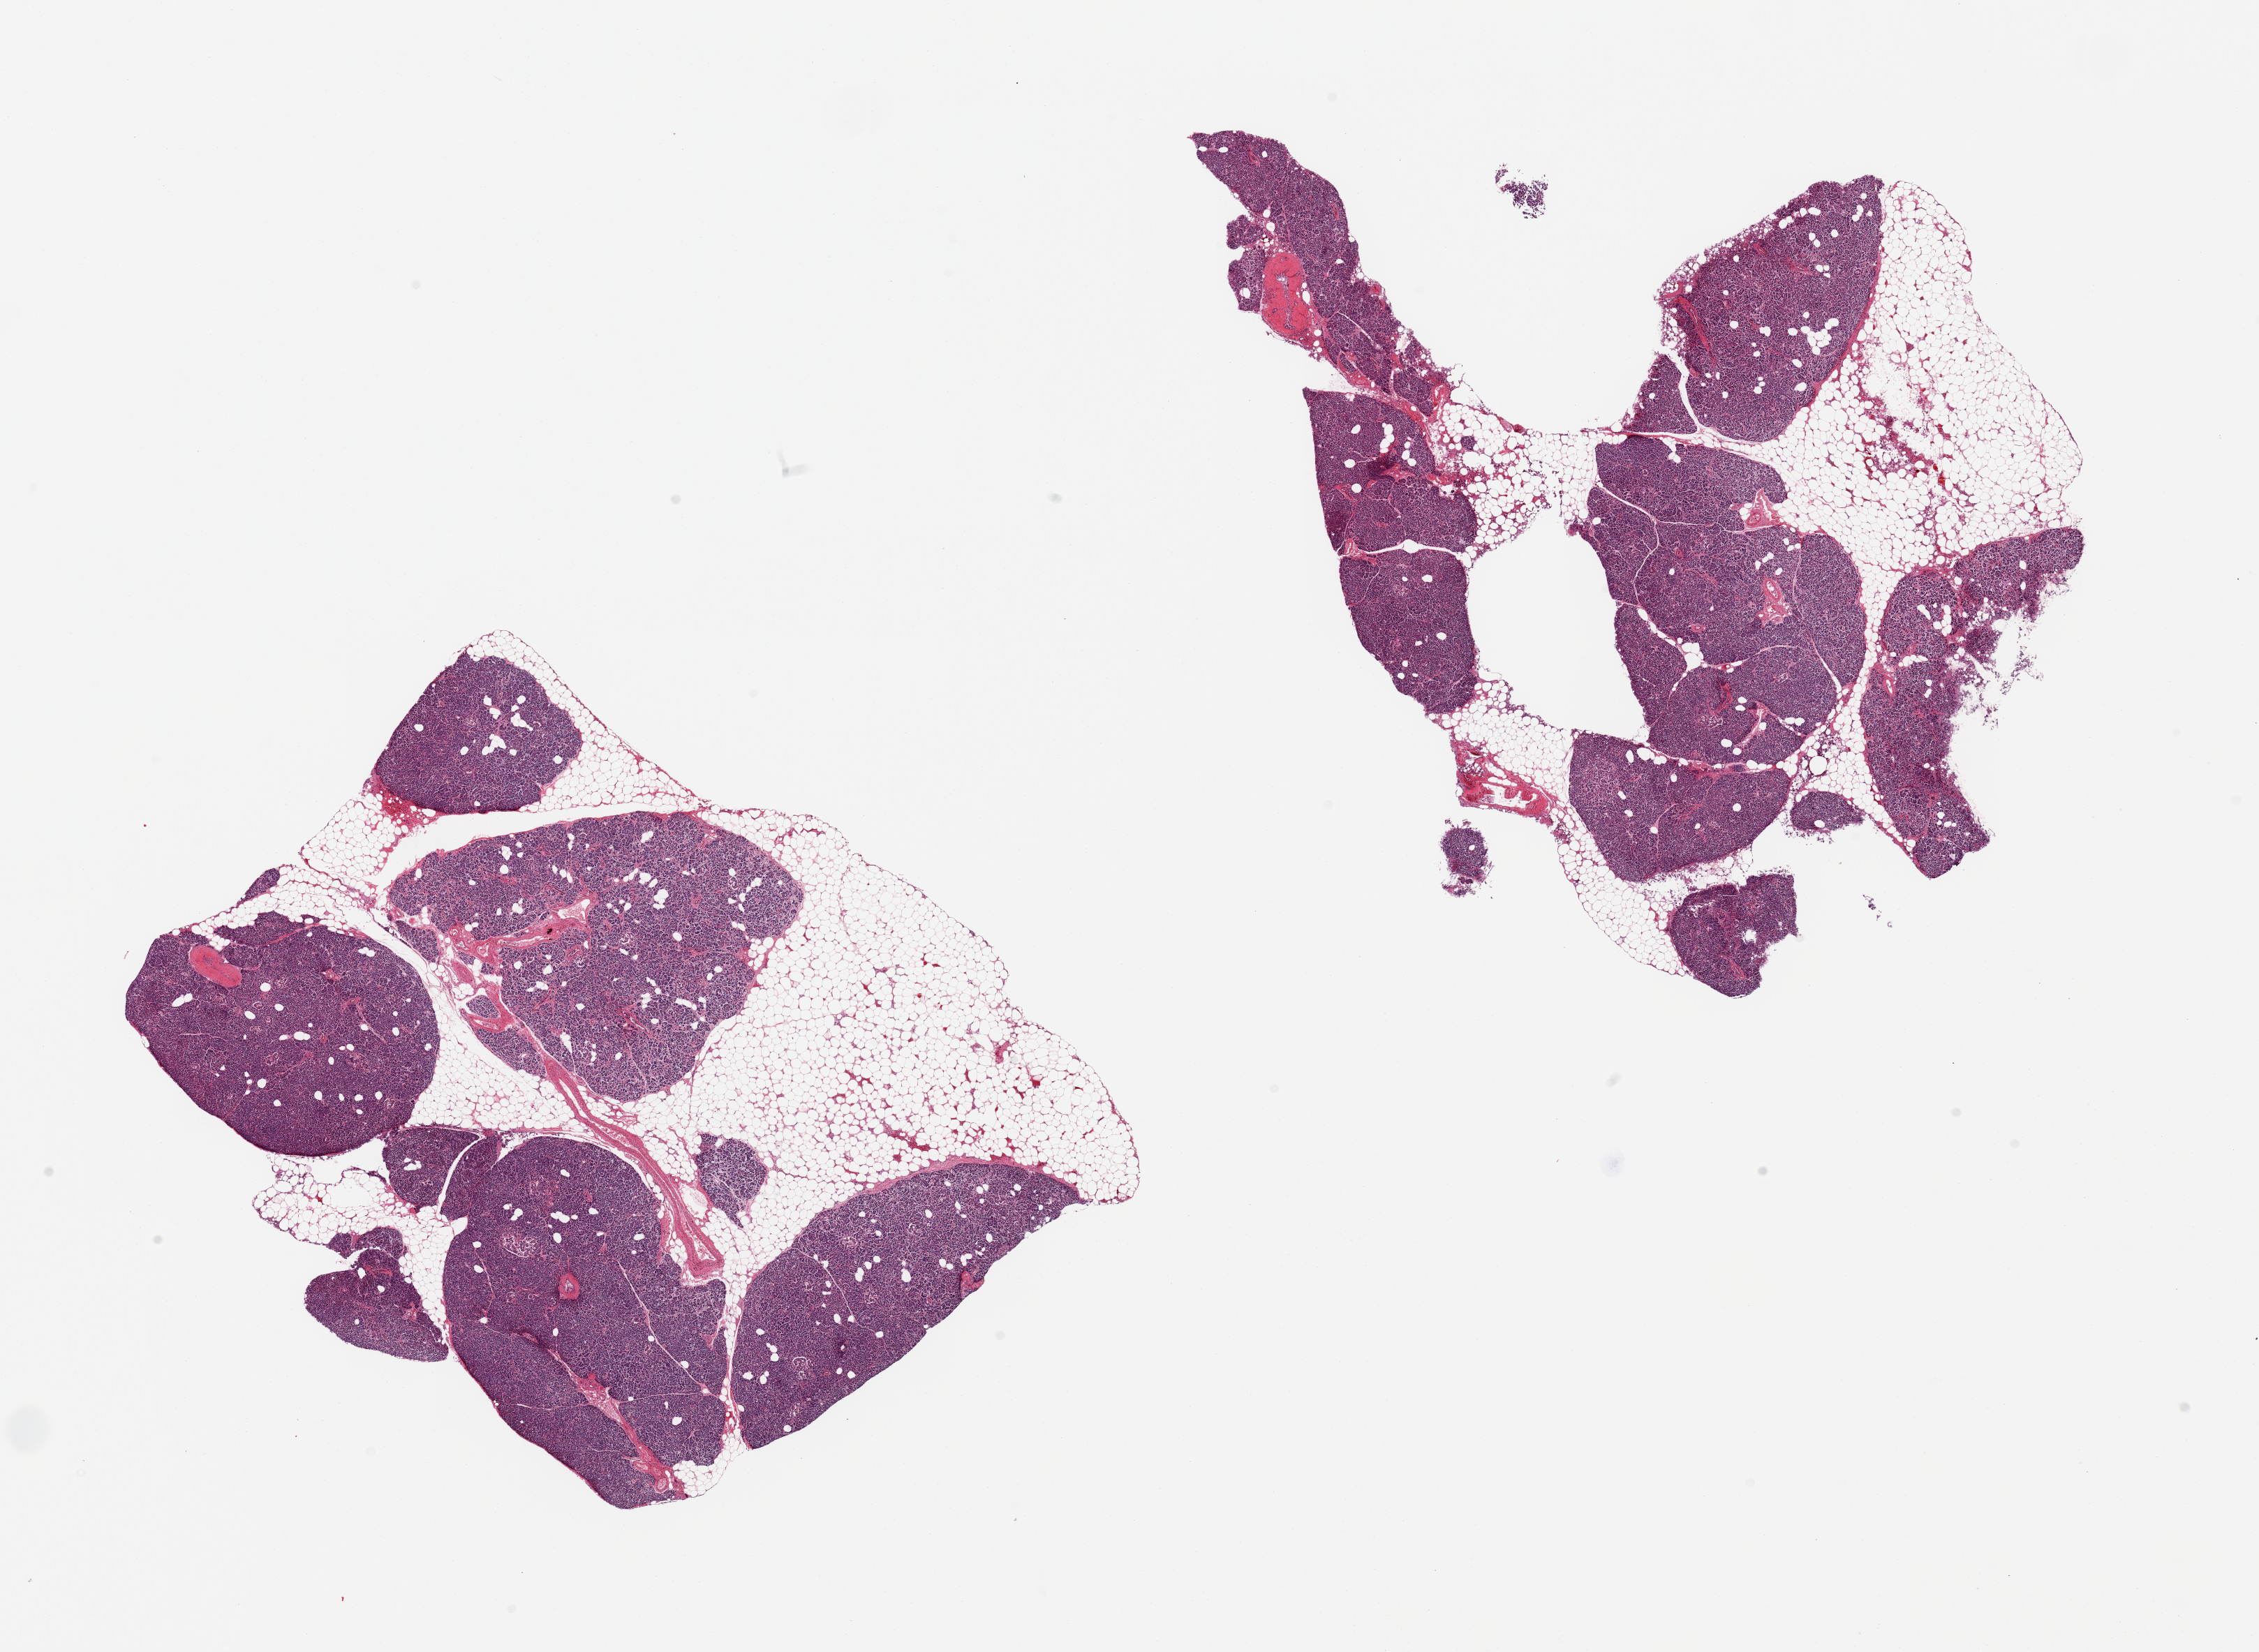
Digitized hematoxylin and eosin (H&E)-stained section — a low-resolution overview of the entire scanned area, about 25.6 x 18.7 mm. PAXgene-fixed, paraffin-embedded tissue. Section of pancreas (target tissue). Tissue donor sample. Donor sex: male.
Pathologist's review note for this sample: 2 pieces; up to 40% of internal/external fat; mild to moderate autolysis; islets of Langerhans visualized.